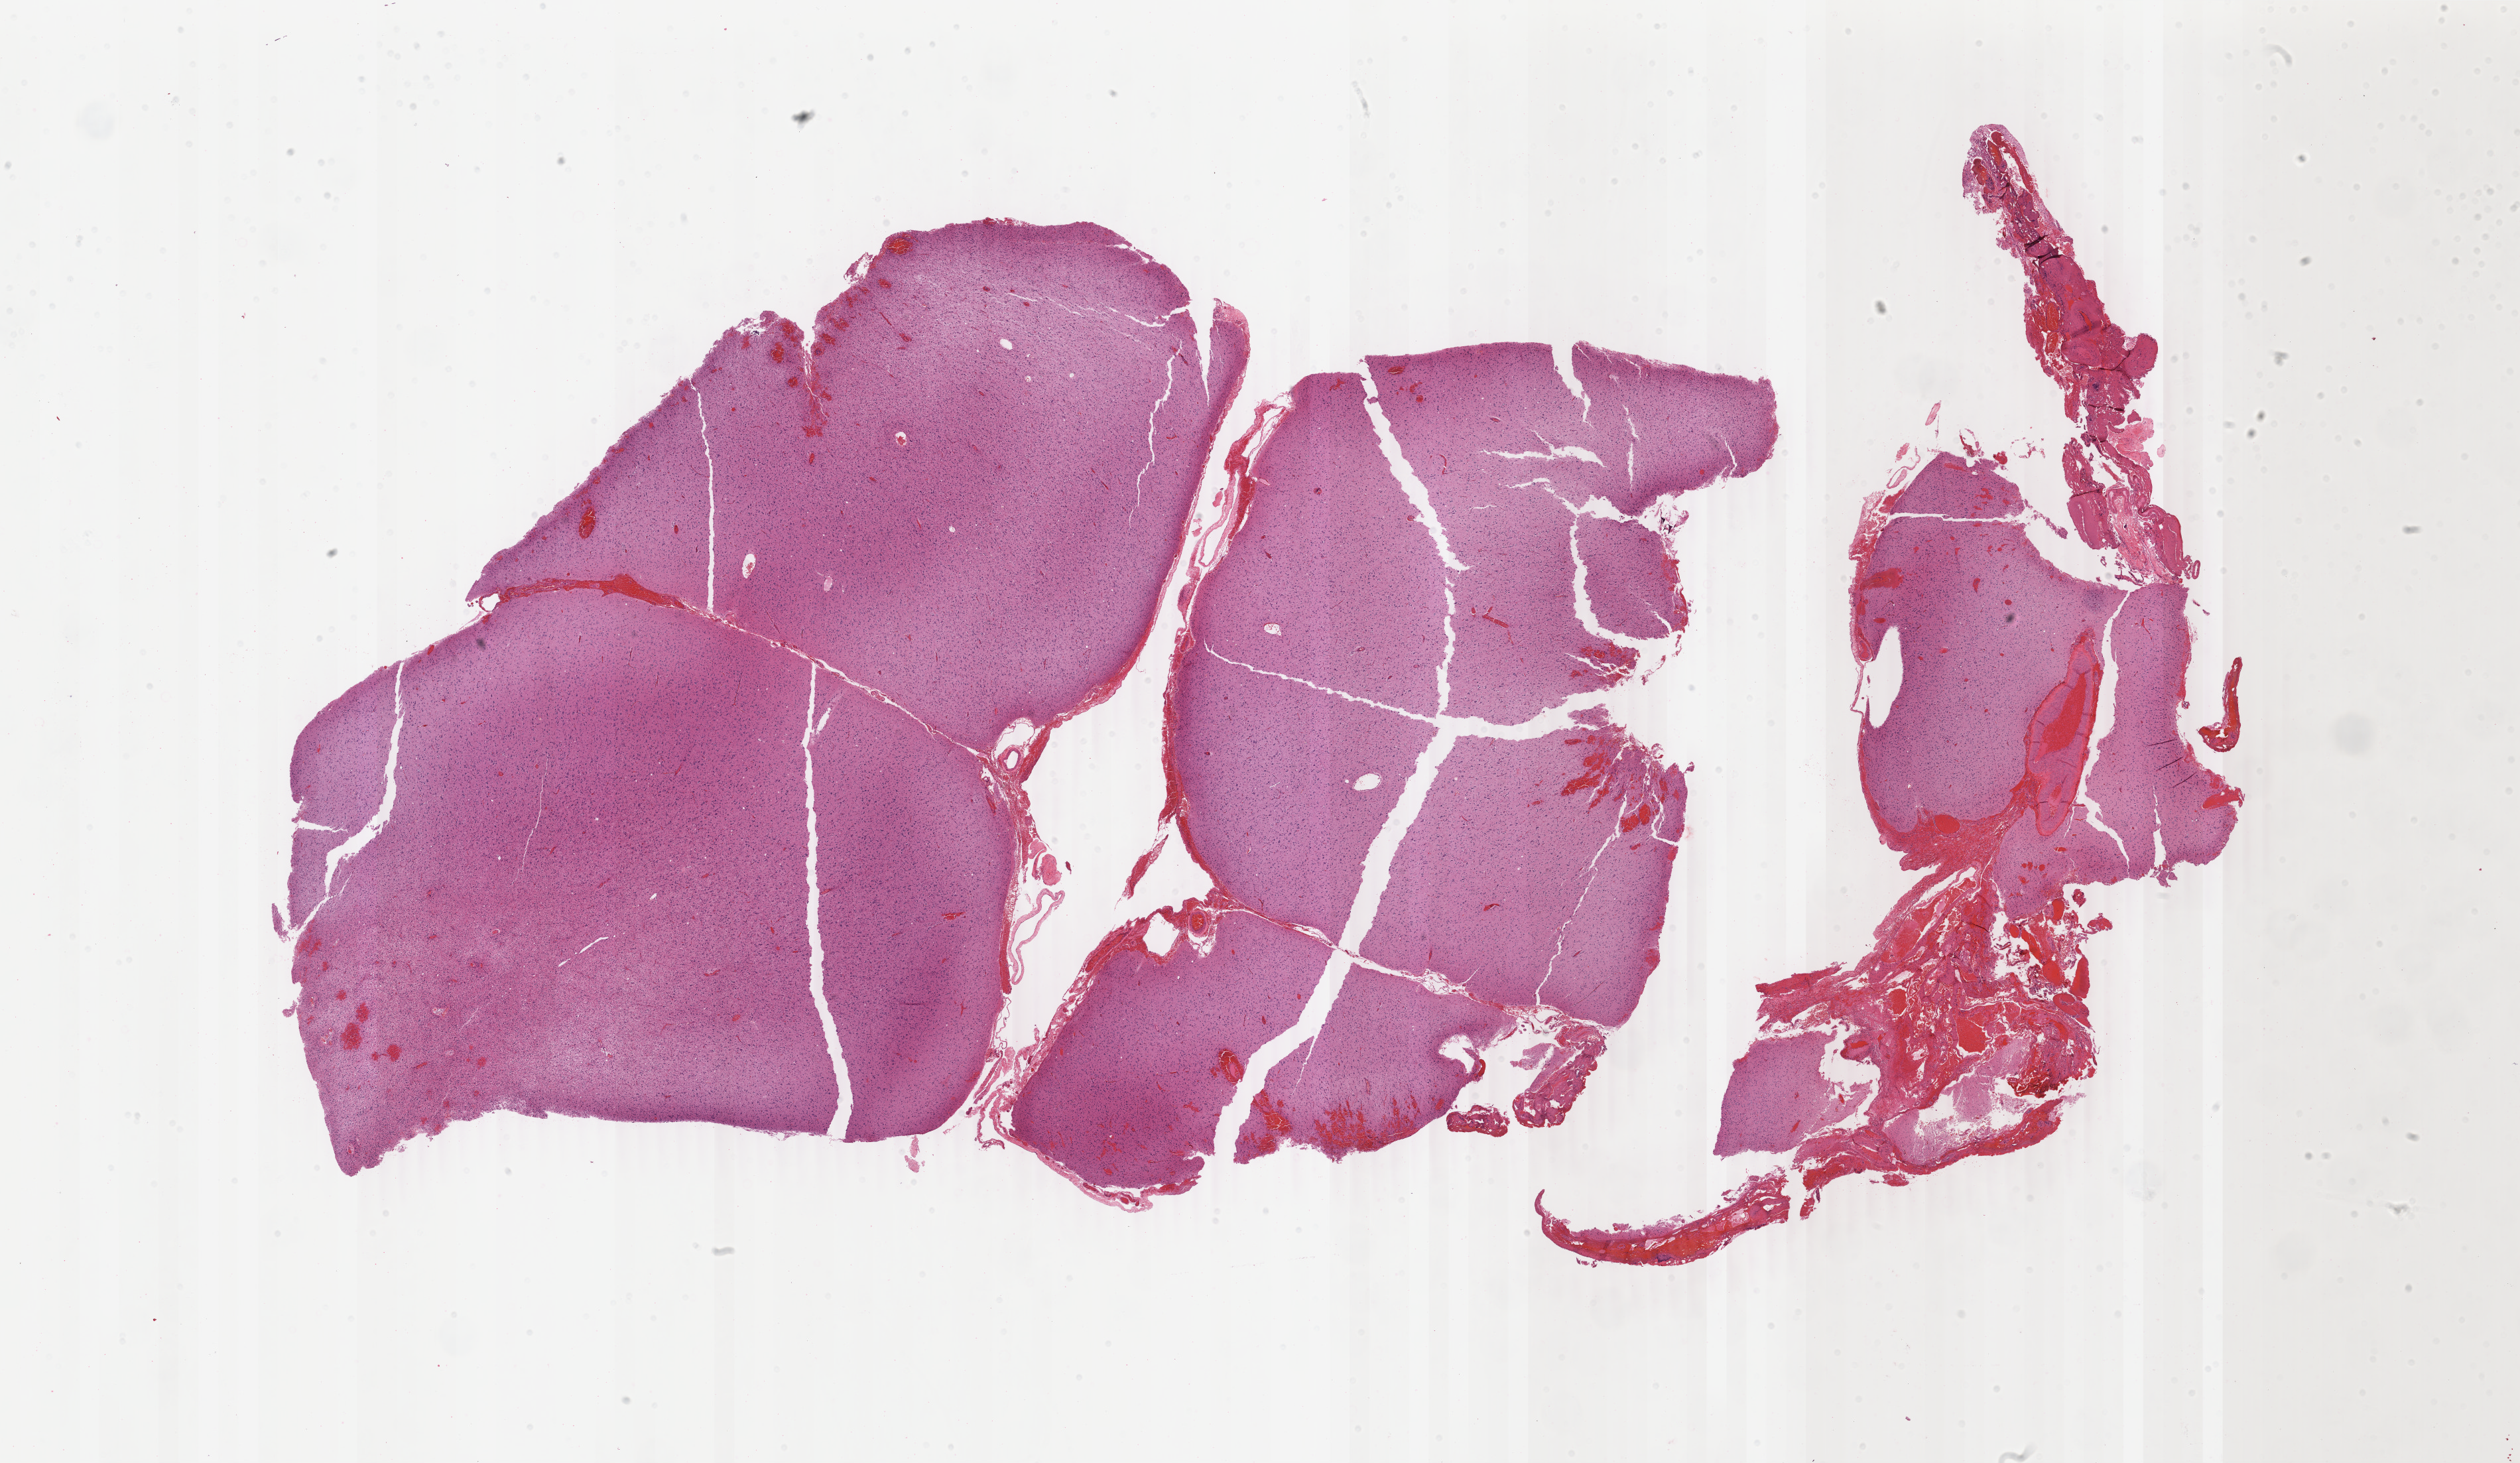
Whole-slide histology image, Hematoxylin and eosin (H&E) stained — a low-resolution overview of the entire scanned area, about 30.2 x 17.5 mm, formalin-fixed paraffin-embedded (FFPE) diagnostic section, brain, primary tumour sample. Male patient; age at initial diagnosis 30 years. Histologic grade: G3 (poorly differentiated).
- histologic diagnosis: Astrocytoma, anaplastic (cerebrum)